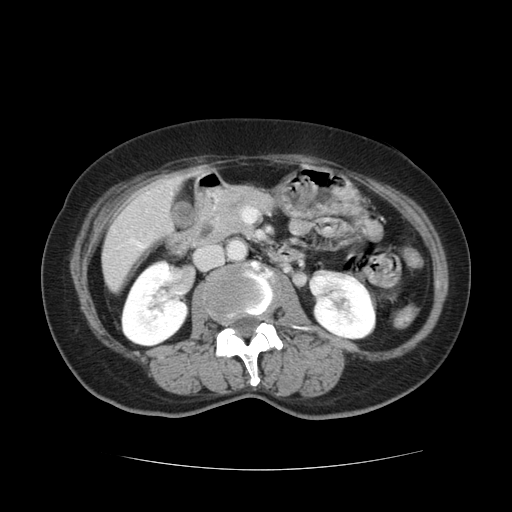
Contrast-enhanced abdominal CT, one axial slice; slice 39 of 128 in the series (ordered by position); 120 kVp; intravenous contrast given; soft-tissue window (W 400 / L 40 HU); 2.5 mm slice thickness; 512 × 512 image matrix, field of view 366 × 366 mm. Female patient, age 67 years. From the clinical record (not read from this slice): diagnosis: colorectal cancer liver metastases, imaged before liver resection; multiple liver metastases: yes; largest metastasis: 3 cm; chemotherapy before resection: no.
Annotated regions visible in this slice (manually delineated by an expert):
- liver: bounding box [x1, y1, x2, y2] px = [103, 175, 181, 289]
- planned liver remnant (the part of the liver to remain after resection): [103, 219, 149, 289]